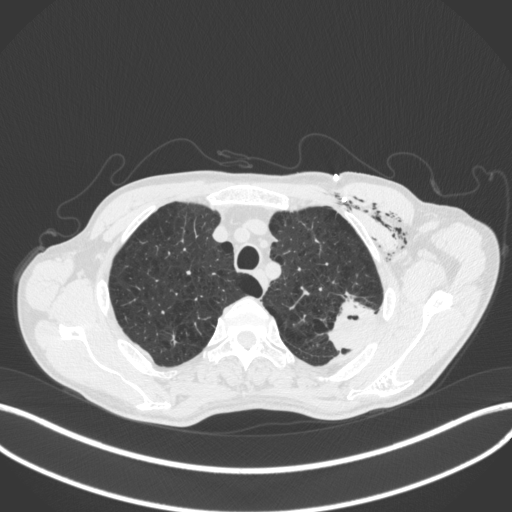
Chest CT, one axial slice. Position 338 of 416 along the scan axis. Lung window (W 1500 / L -600 HU). 1 mm slice thickness. 512 × 512 image matrix, field of view 400 × 400 mm. Male patient, age 58 years. Case-level facts recorded for this patient, not image findings: clinical TNM (as recorded): T3 N0 M0.
Structures marked on this image (bounding box drawn by a radiologist):
- lung tumour (recorded histology: adenocarcinoma): box from (x=325, y=293) to (x=380, y=353) px